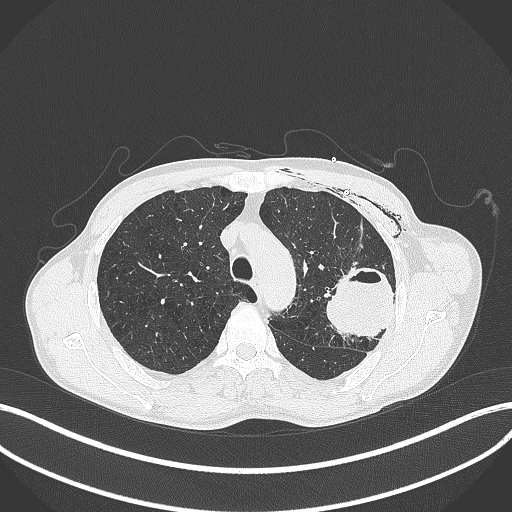
Chest CT, one axial slice. Position 303 of 457 along the scan axis. 120 kVp. Lung window (W 1500 / L -600 HU). 512 × 512 image matrix, field of view 400 × 400 mm. Patient: male, 58 years. Case-level facts recorded for this patient, not image findings: clinical TNM (as recorded): T3 N0 M0.
Annotated regions visible in this slice (rectangle marked by the reading radiologist):
- lung tumour (recorded histology: adenocarcinoma): bounding box (x1, y1, x2, y2) in pixels: (325, 266, 394, 343)